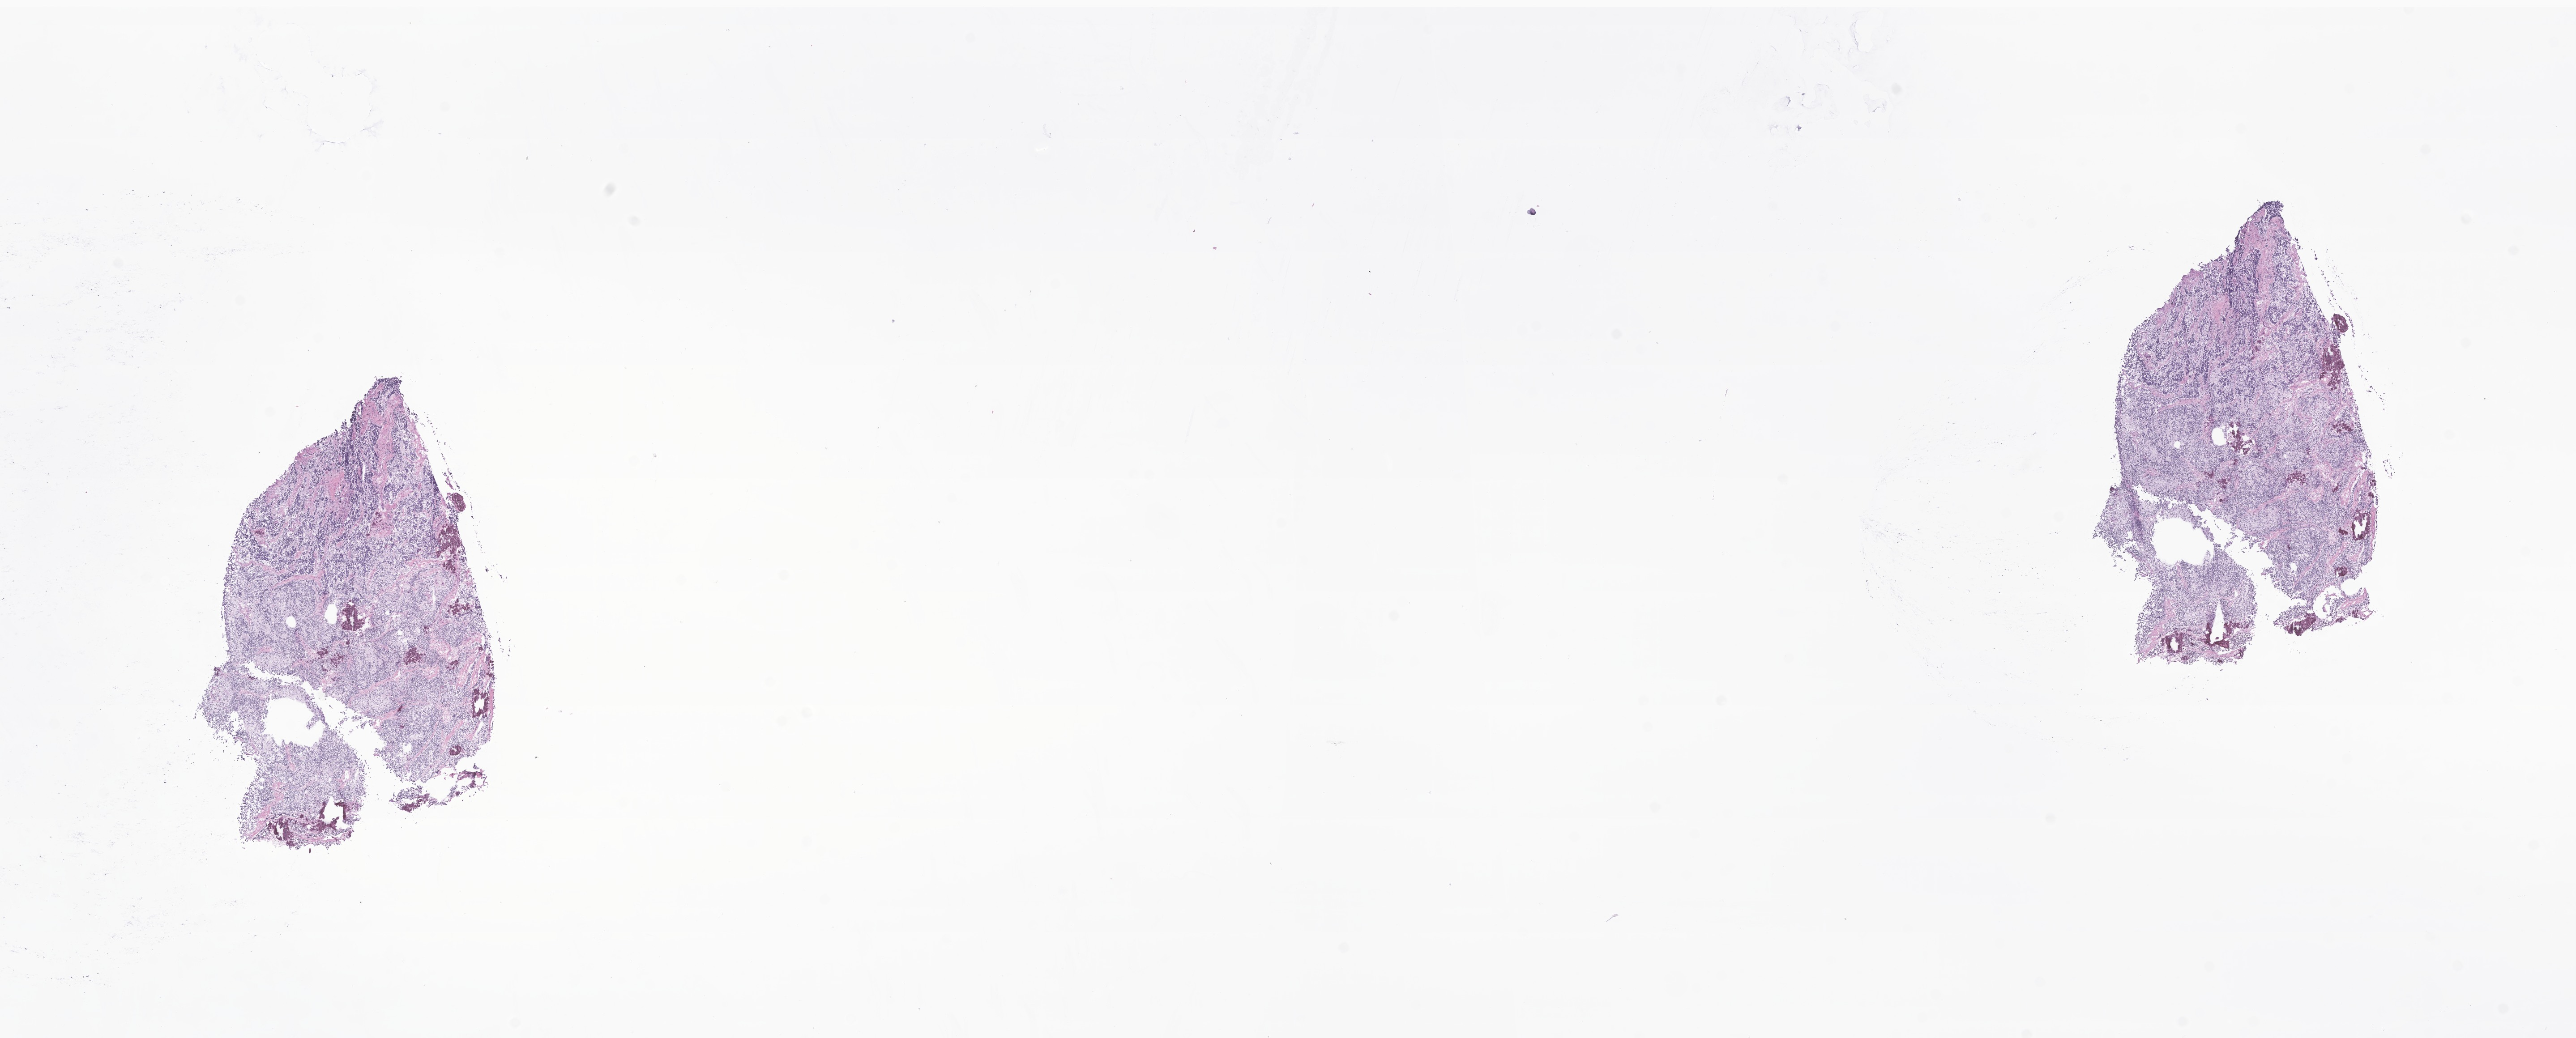
Whole-slide image, hematoxylin and eosin (H&E) stain of tumor tissue from the thorax — shown as a low-resolution overview of the whole scanned area (about 24.3 x 9.8 mm). Frozen section. Male patient, age 28 days.
- diagnosis (ICD-O-3 morphology term): Neuroblastoma, NOS